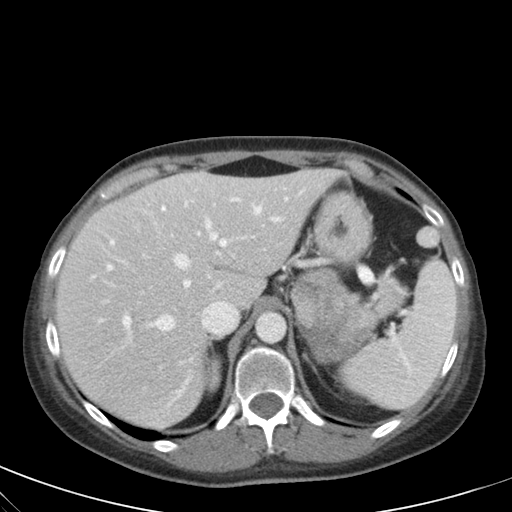
Contrast-enhanced abdominal CT, one axial slice. Slice 44 of 59 in the series (ordered by position). 120 kVp. Intravenous contrast given. Soft-tissue window (W 400 / L 40 HU). 512 × 512 image matrix. Patient: female, 28 years. Case-level facts recorded for this patient, not image findings: diagnosis: adrenocortical carcinoma; tumour side: left adrenal; tumour size at pathology: 7 cm; Ki-67 index: 40 %.
Annotated regions visible in this slice (semi-automatically segmented with operator editing):
- mass: bounding box <292,269,375,363> (left, top, right, bottom; pixels)